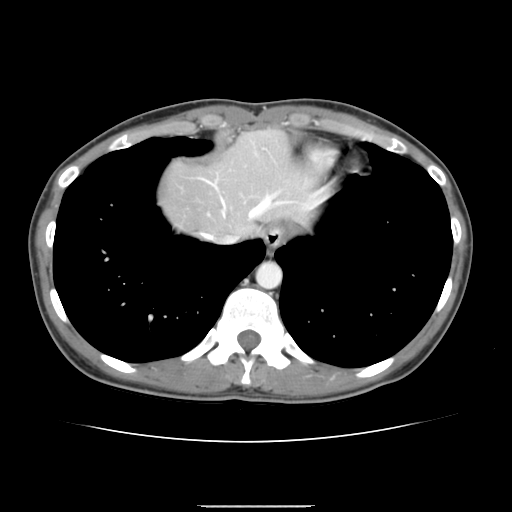
Contrast-enhanced abdominal CT, one axial slice. Slice 130 of 150 in the series (ordered by position). 120 kVp. Intravenous contrast given. Soft-tissue window (W 400 / L 40 HU). 512 × 512 image matrix. Female patient, age 32 years. Case-level facts recorded for this patient, not image findings: diagnosis: colorectal cancer liver metastases, imaged before liver resection; multiple liver metastases: yes; largest metastasis: 0.7 cm; disease in both lobes: no.
Structures marked on this image (manually delineated by an expert):
- hepatic veins: box from (x=202, y=180) to (x=285, y=243) px
- liver: (x=161, y=130)–(x=321, y=235)
- planned liver remnant (the part of the liver to remain after resection): (x=161, y=130)–(x=321, y=236)